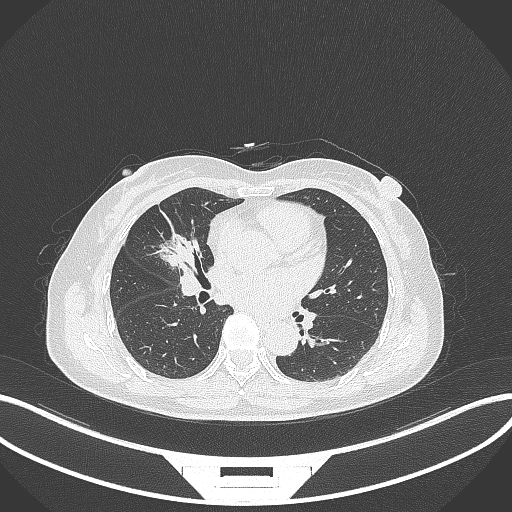
Chest CT, one axial slice. Slice 150 of 284 in the series (ordered by position). 120 kVp. Lung window (W 1500 / L -600 HU). 512 × 512 image matrix. Female patient, age 51 years. From the clinical record (not read from this slice): clinical TNM (as recorded): T1c N0 M0.
Outlined on this slice (rectangle marked by the reading radiologist):
- lung tumour (recorded histology: adenocarcinoma): bounding box (x1, y1, x2, y2) in pixels: (156, 232, 205, 274)